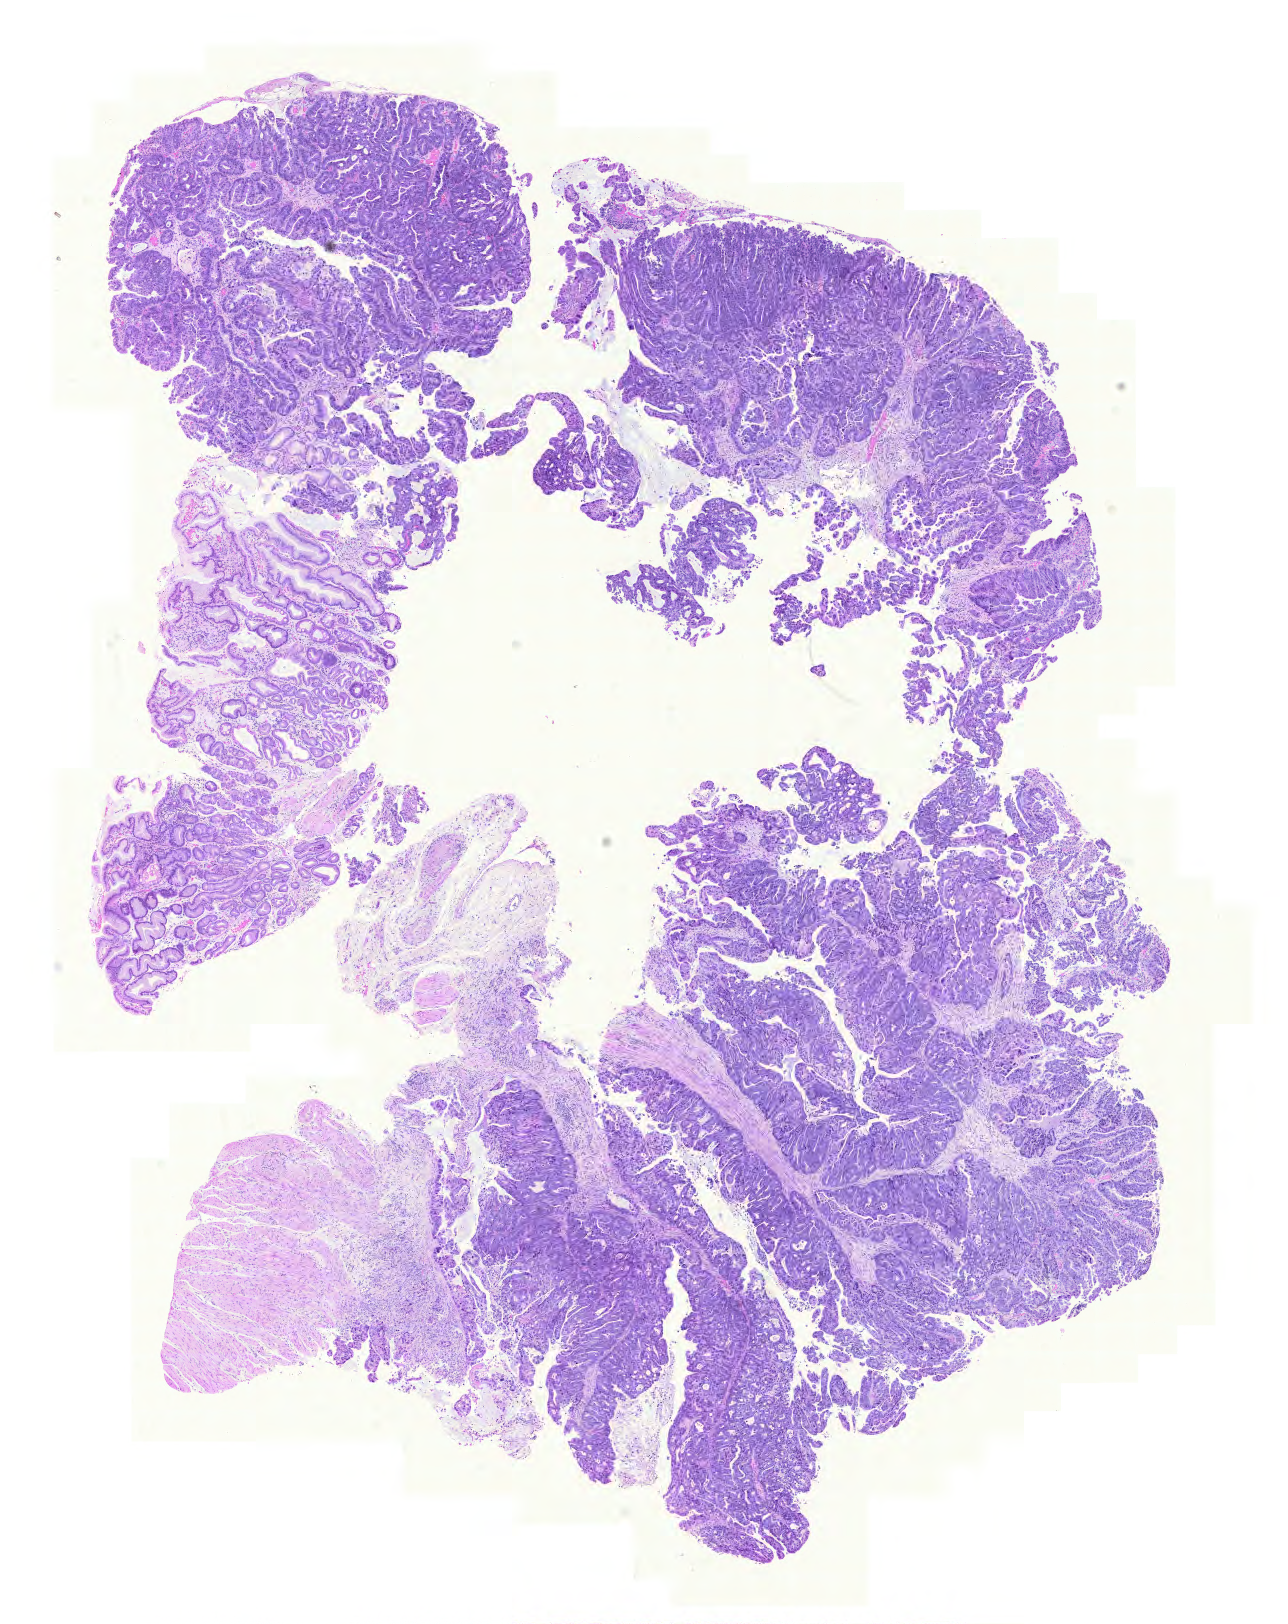
Hematoxylin and eosin (H&E) stained whole-slide image, a low-resolution overview of the entire scanned area, about 9.6 x 12.1 mm (acquisition: 20x scan). Formalin-fixed paraffin-embedded (FFPE) diagnostic section. Primary tumour sample from the stomach. Patient: female, age at initial diagnosis 81 years. Histologic grade: G2 (moderately differentiated).
* AJCC pathologic stage: IB
* pathologic diagnosis: Adenocarcinoma, intestinal type (cardia, NOS)